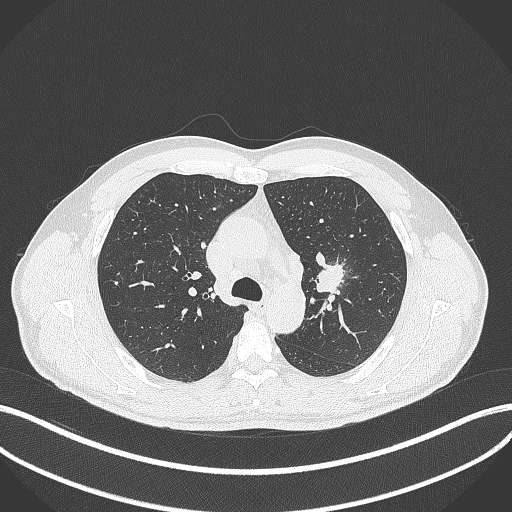
Chest CT, one axial slice; position 291 of 392 along the scan axis; lung window (W 1500 / L -600 HU); 1 mm slice thickness; 512 × 512 image matrix, field of view 400 × 400 mm. Male patient, age 50 years. Case-level facts recorded for this patient, not image findings: clinical TNM (as recorded): T1c N1 M1b.
Outlined on this slice (rectangle marked by the reading radiologist):
- lung tumour (recorded histology: squamous cell carcinoma): box from (x=314, y=257) to (x=349, y=296) px